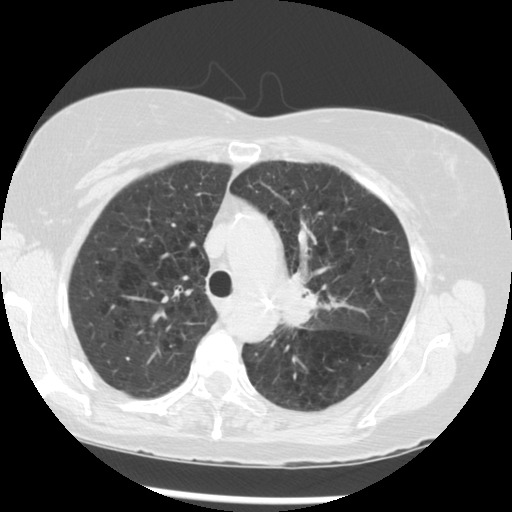
Low-dose screening chest CT, one axial slice; position 209 of 283 along the scan axis; reconstruction kernel STANDARD; lung window (W 1500 / L -600 HU); 512 × 512 image matrix, field of view 330 × 330 mm.
Structures marked on this image (expert manual segmentation):
- lesion 1 (tumor, upper lobe of left lung): bounding box <280,275,319,327> (left, top, right, bottom; pixels)